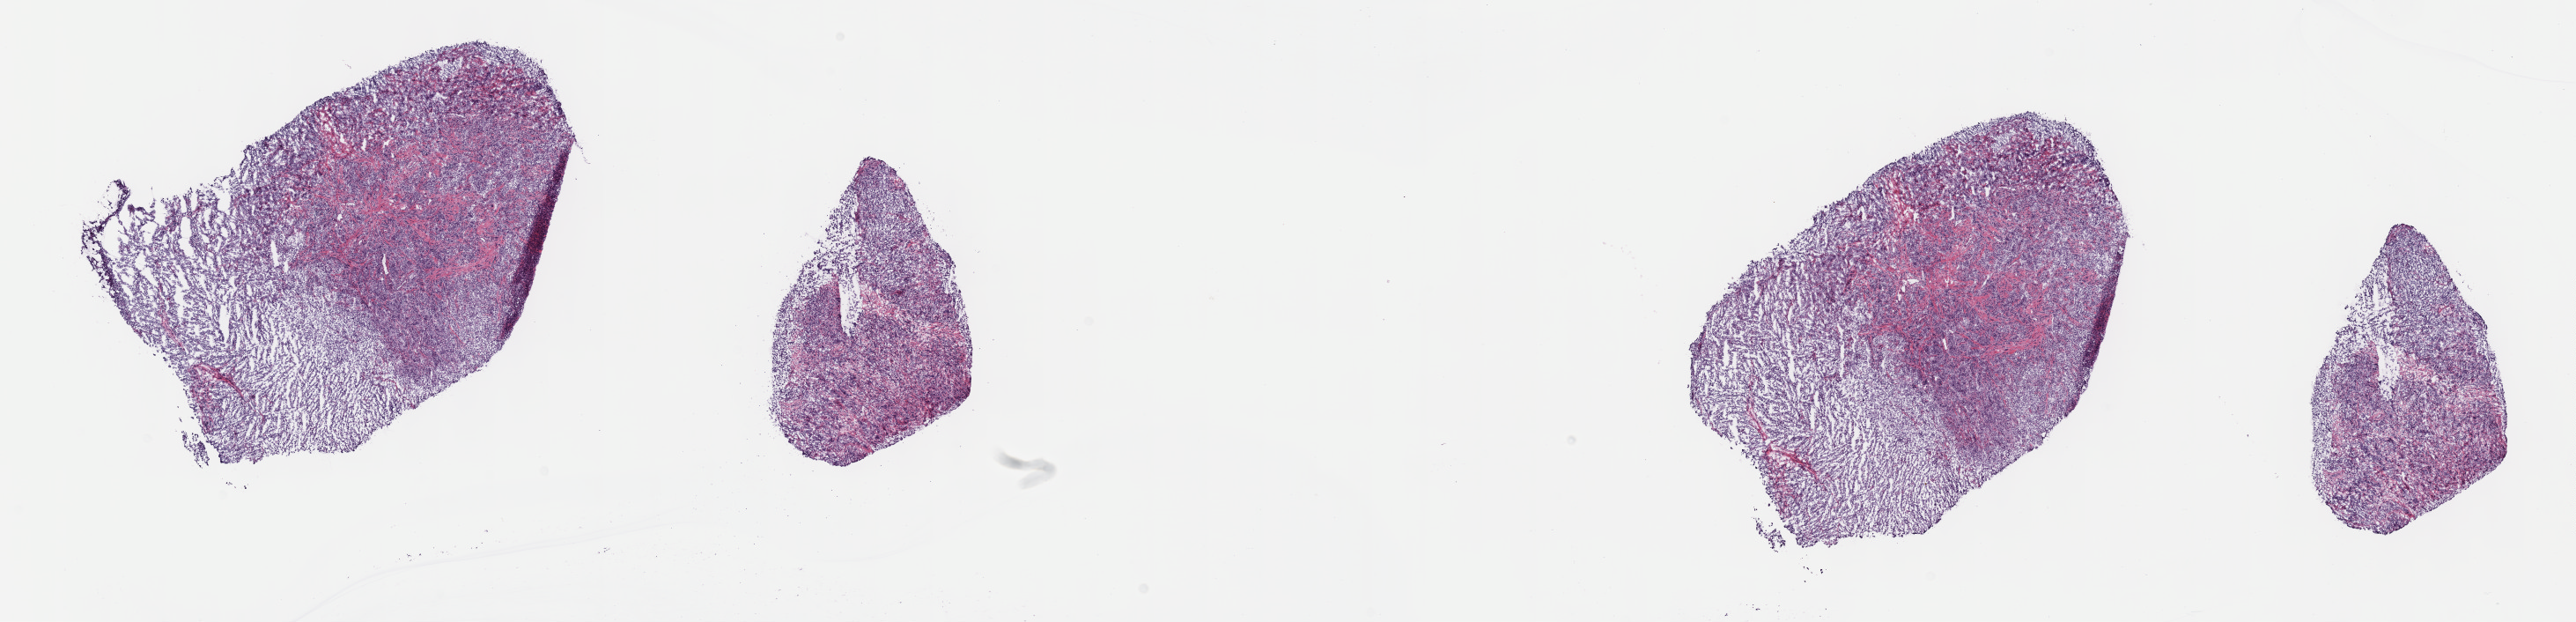
Digitized Hematoxylin and eosin (H&E) stained tissue section (whole slide) — low-resolution overview of the scanned area, about 23.7 x 5.7 mm (acquisition: 40x scan), frozen section, primary tumour sample from the testis. Male, age 42 years at initial diagnosis. Pathologist review of this section (percent, as recorded): tumour cells 85%, tumour nuclei 90%, normal cells 0%, stromal cells 15%, necrosis 0%. Inflammatory infiltration, as recorded: lymphocyte infiltration 0%, monocyte infiltration 0%, neutrophil infiltration 0%.
* AJCC pathologic stage: I (7th edition)
* TNM: T1 NX M0
* histologic diagnosis: Seminoma, NOS